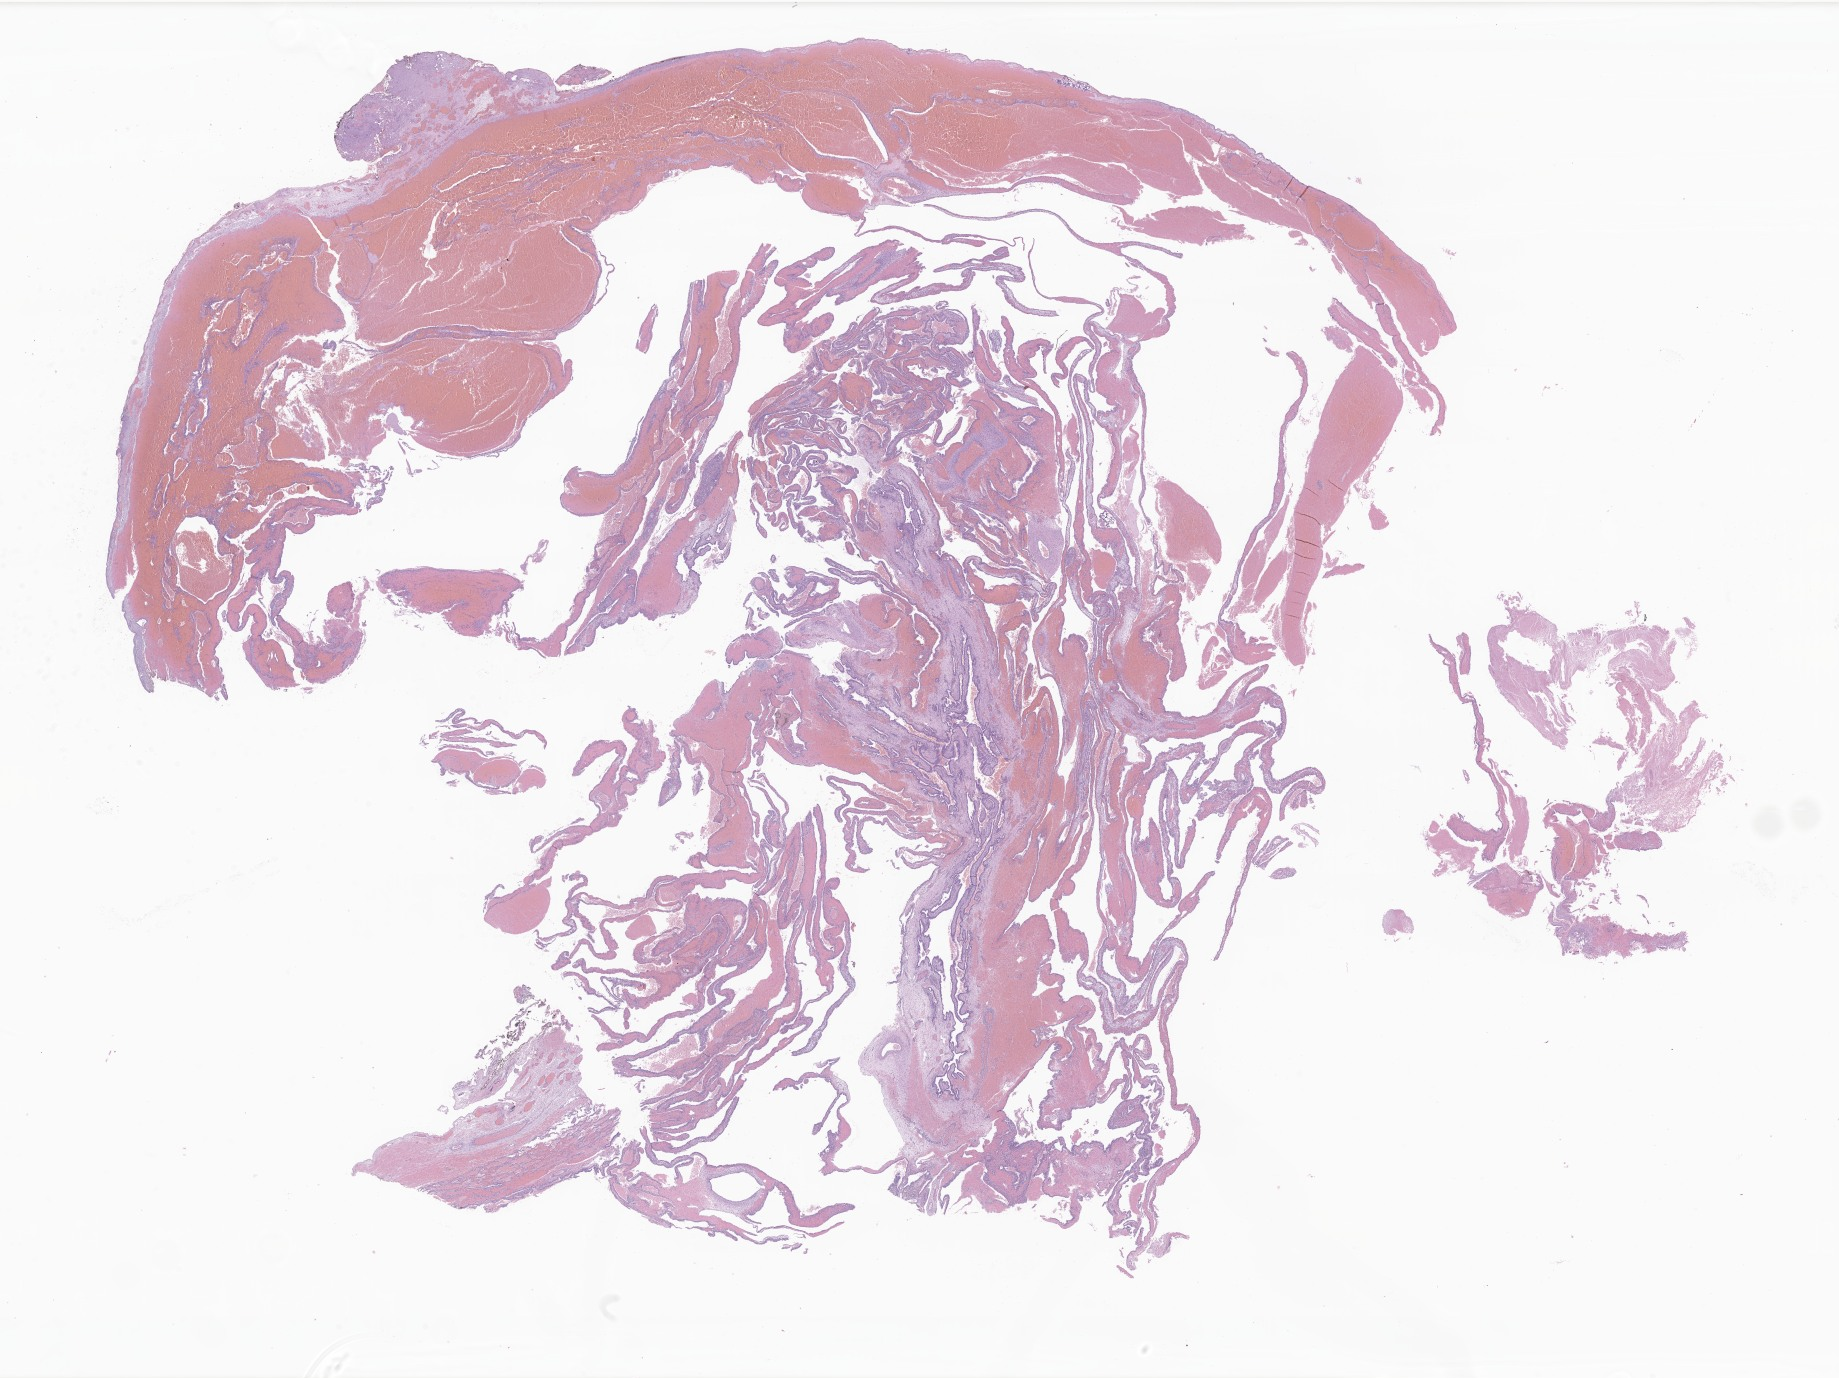
Digitized H&E-stained section of tumor tissue from the lower lobe of lung, low-resolution overview of the scanned area, about 31.0 x 23.2 mm. Formalin-fixed paraffin-embedded section. Patient: male, age 30 days.
- diagnosis: Pleuropulmonary blastoma
- tissue or organ of origin (case record): lower lobe, lung